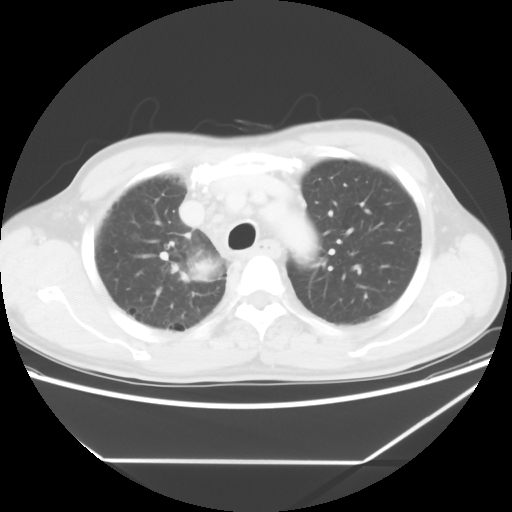
Chest CT, one axial slice; position 46 of 60 along the scan axis; reconstruction kernel STANDARD; lung window (W 1500 / L -600 HU); 512 × 512 image matrix, field of view 367 × 367 mm. Male patient, age 58 years. From the clinical record (not read from this slice): clinical TNM (as recorded): T2 N2 M0.
Outlined on this slice (rectangle marked by the reading radiologist):
- lung tumour (recorded histology: squamous cell carcinoma): bounding box [x1, y1, x2, y2] px = [187, 258, 216, 291]